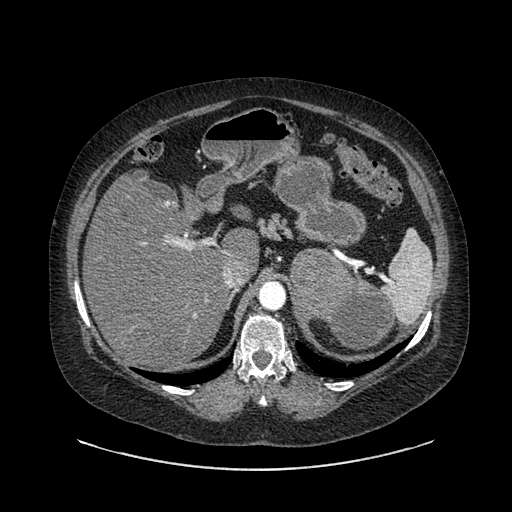
Contrast-enhanced abdominal CT, one axial slice; position 606 of 769 along the scan axis; reconstruction kernel SOFT; soft-tissue window (W 400 / L 40 HU); 0.62 mm slice thickness; 512 × 512 image matrix, field of view 460 × 460 mm. Female patient, age 61 years. From the clinical record (not read from this slice): diagnosis: adrenocortical carcinoma; tumour side: left adrenal; tumour size at pathology: 13 cm; Ki-67 index: 79 %; stage (as recorded): 2.
Structures marked on this image (semi-automatically segmented with operator editing):
- mass: bounding box <290,253,393,350> (left, top, right, bottom; pixels)